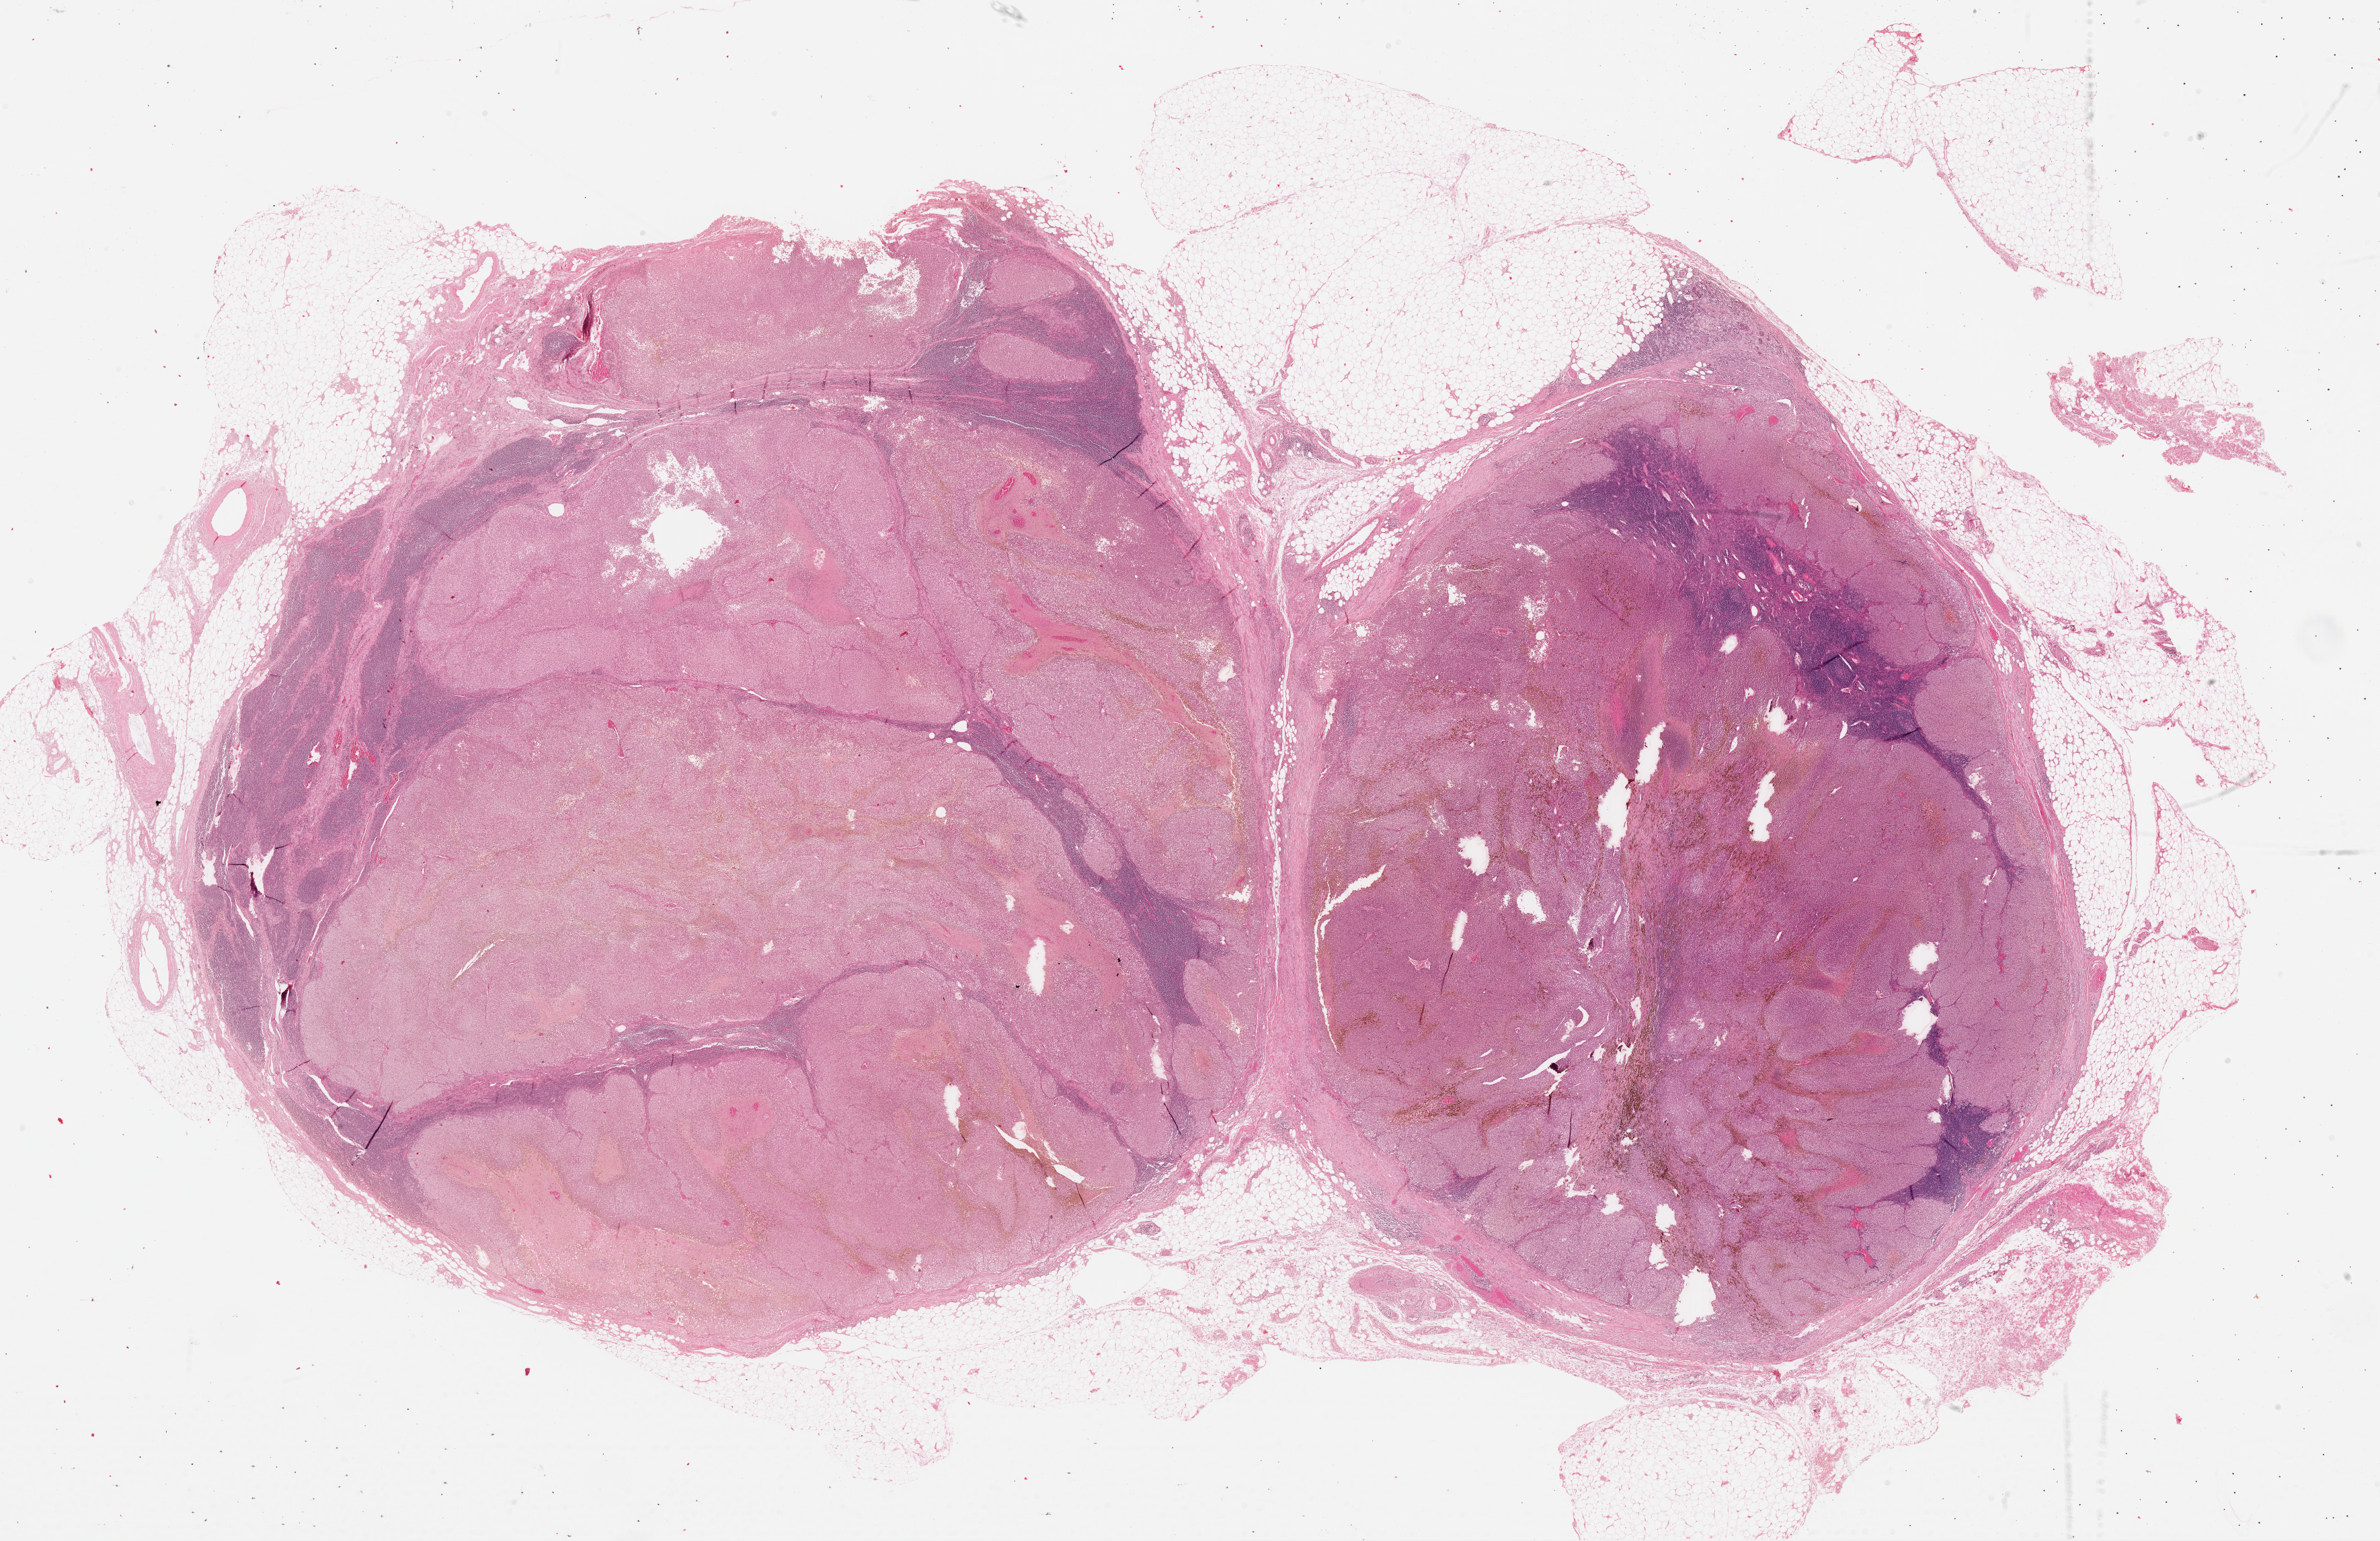
H&E-stained whole-slide image — shown as a low-resolution overview of the whole scanned area (about 28.0 x 18.1 mm). Formalin-fixed paraffin-embedded (FFPE) diagnostic section. Primary tumour sample from the skin. Male, age 30 years at initial diagnosis.
Histologic diagnosis: Malignant melanoma, NOS.